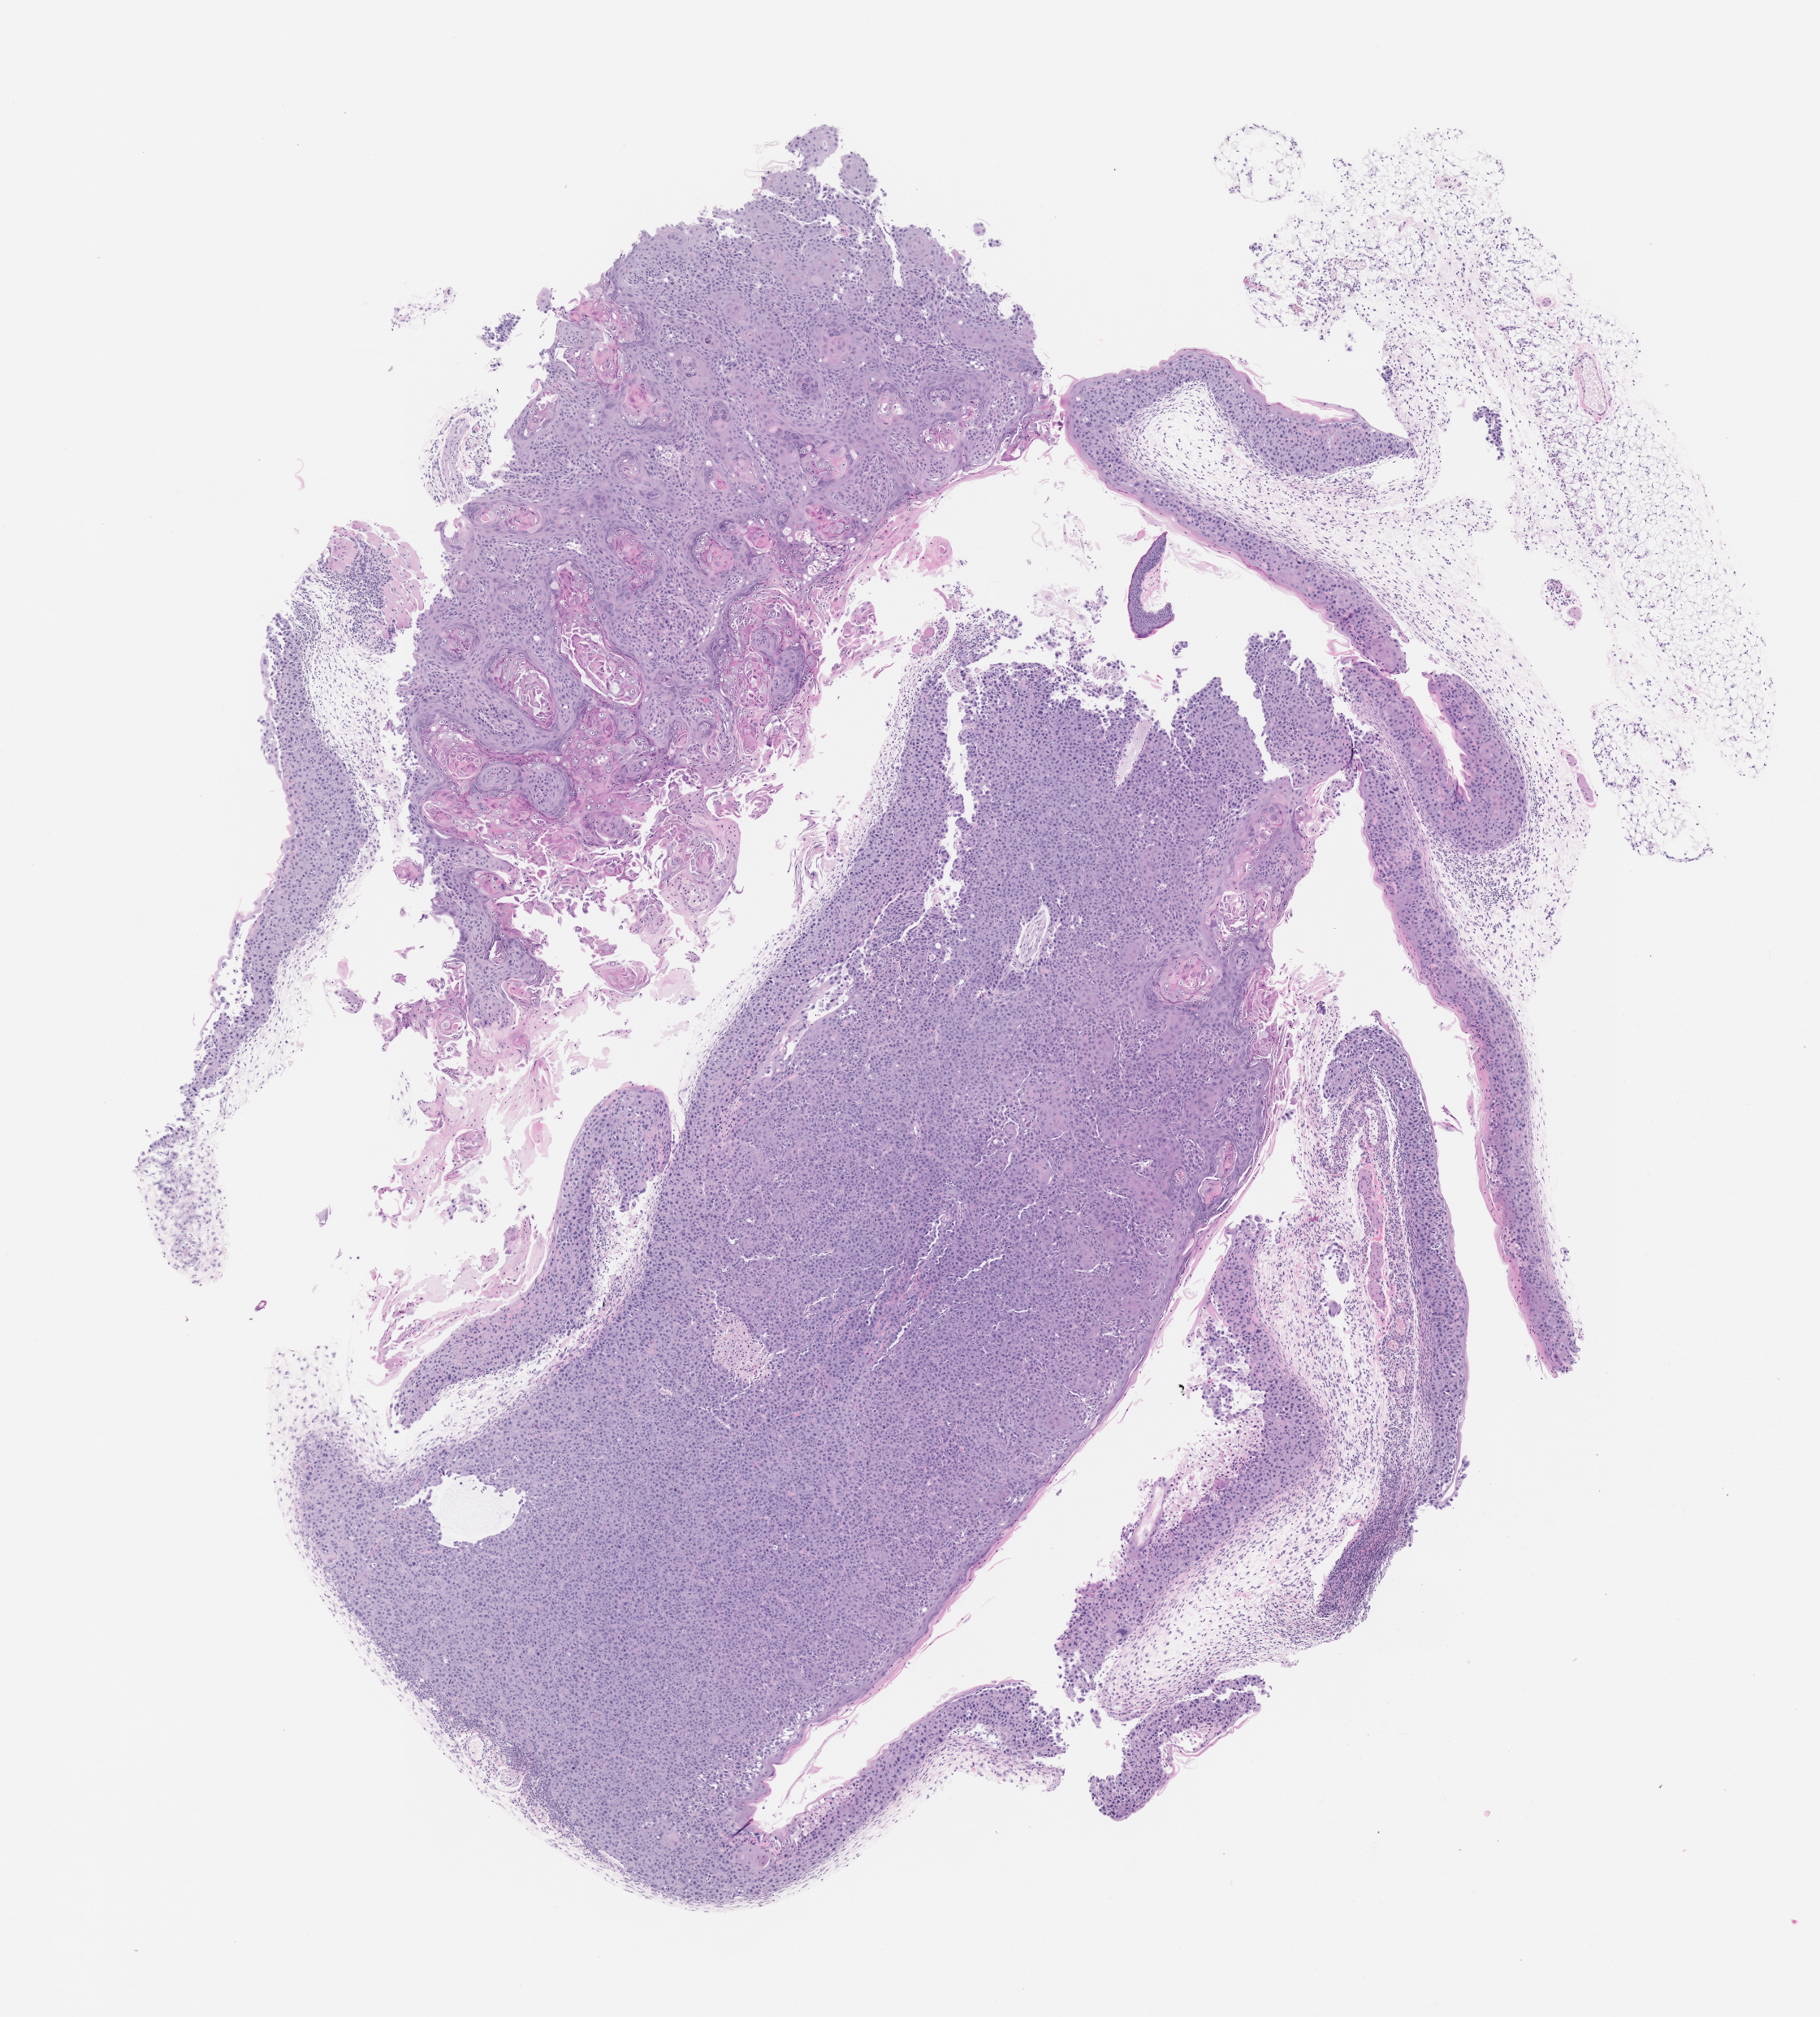
H&E whole-slide image of a patient-derived xenograft (PDX) tumor grown in a mouse, passage 3 — a low-resolution overview of the entire scanned area, about 9.0 x 10.0 mm; FFPE section; tumor site category: oral soft tissue.
Originating patient diagnosis: Head and Neck Squamous Cell Carcinoma.